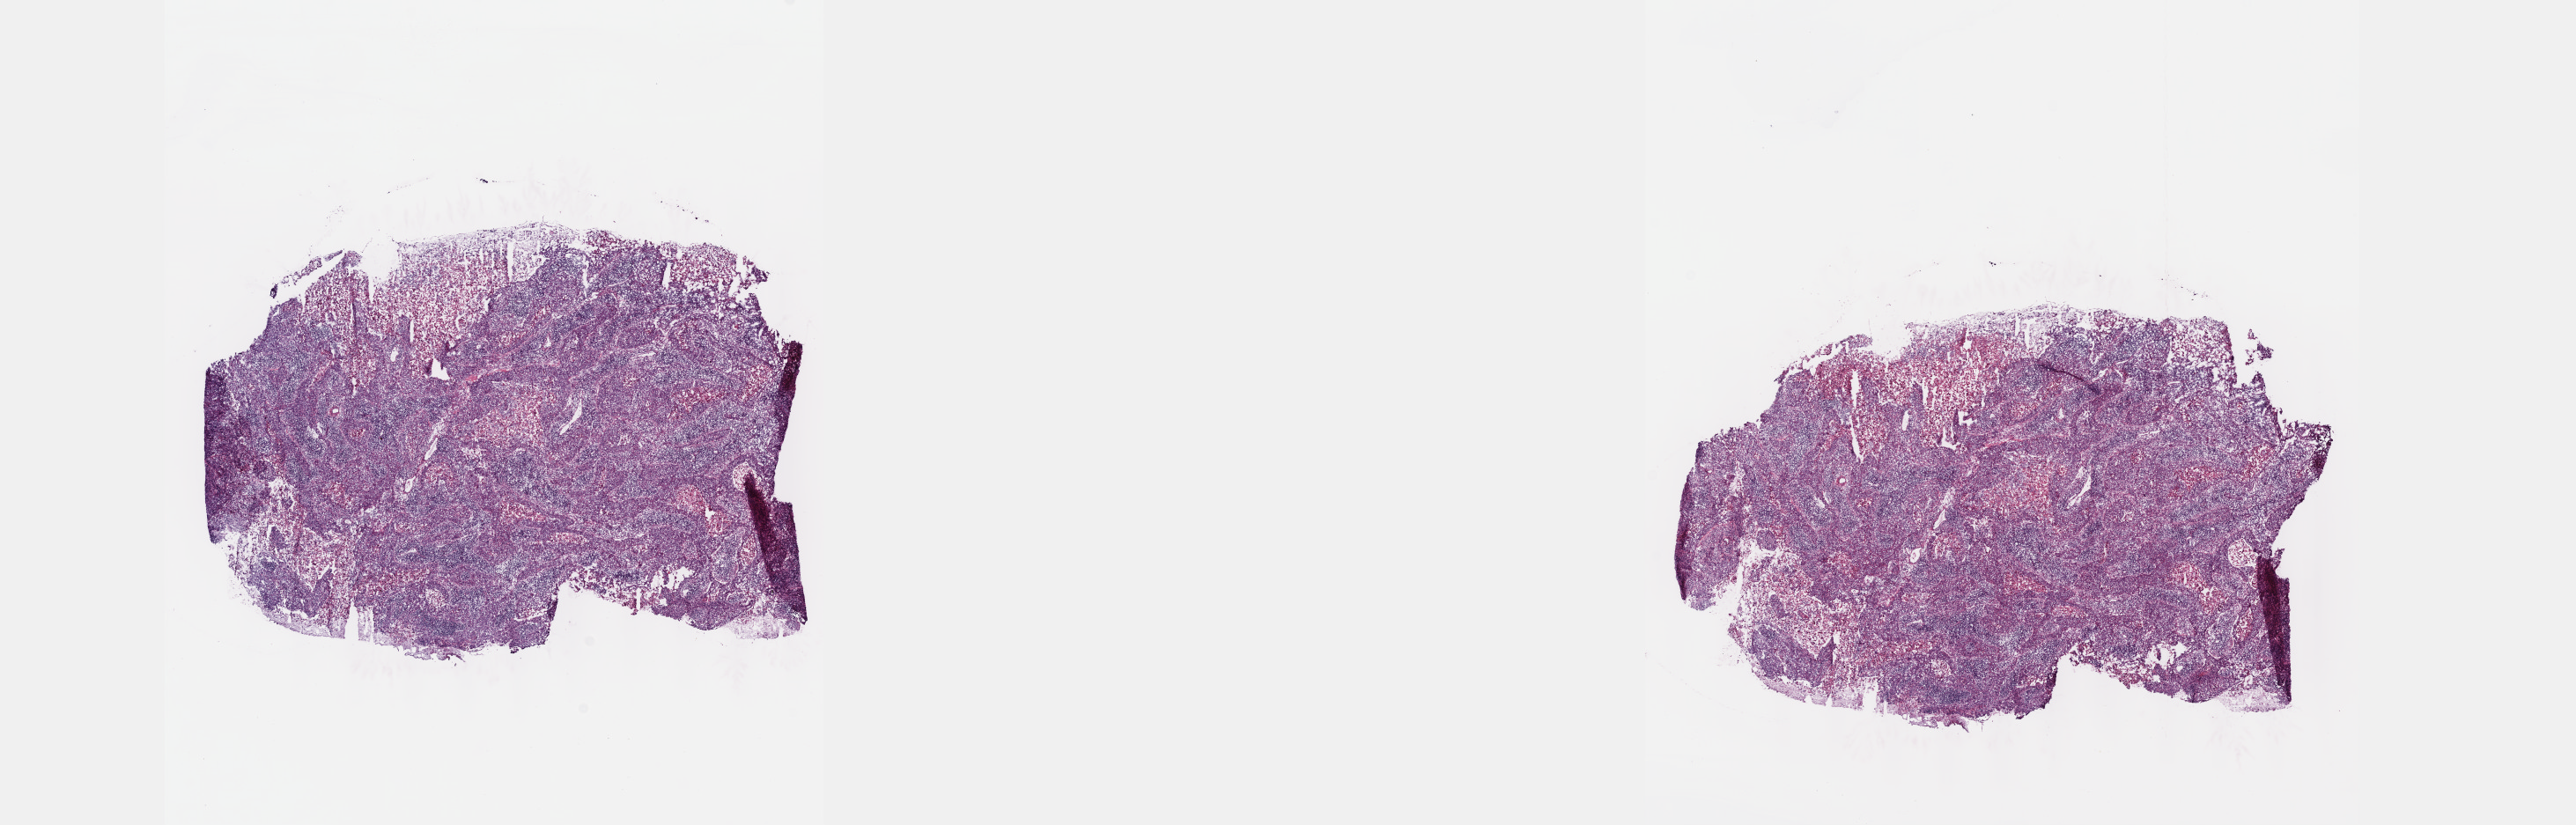
Whole-slide histology image, Hematoxylin and eosin (H&E) stained, a low-resolution overview of the entire scanned area, about 23.6 x 7.6 mm (acquisition: 40x scan); frozen section; sample: primary tumour, cervix. Patient: female, age at initial diagnosis 70 years. Histologic grade: G2 (moderately differentiated). Composition of this section per pathologist review: tumour cells 60%, tumour nuclei 60%, normal cells 0%, stromal cells 39%, necrosis 1%. Inflammatory infiltration, as recorded: lymphocyte infiltration 10%, monocyte infiltration 5%, neutrophil infiltration 5%.
FIGO stage: IIIB. Diagnosis: Squamous cell carcinoma, large cell, nonkeratinizing, NOS (cervix uteri).